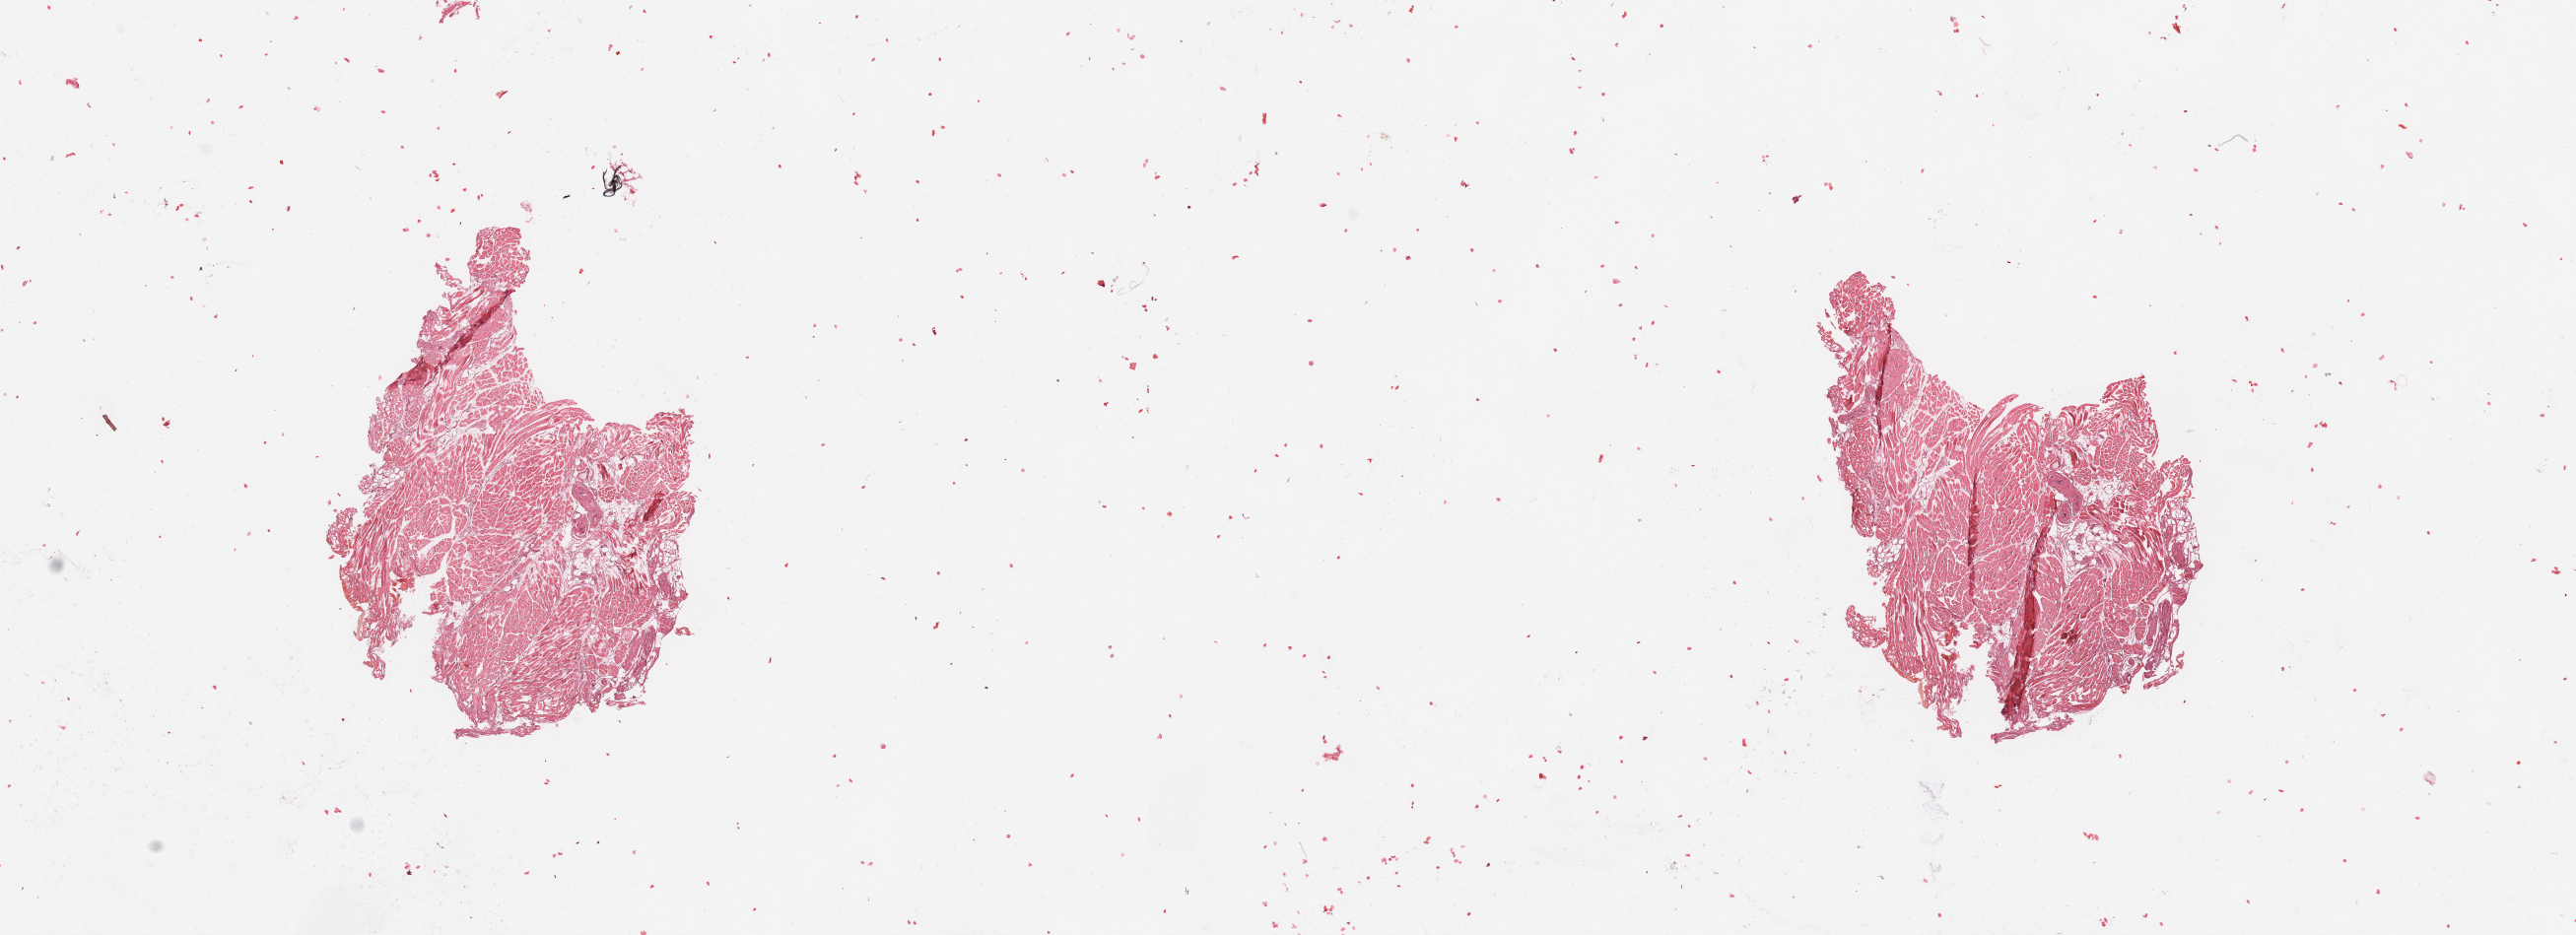
Digitized Hematoxylin and eosin (H&E) stained tissue section (whole slide) — whole scanned area (about 20.7 x 7.5 mm, acquisition: 20x scan) shown as a low-resolution overview, head and neck, tissue type not recorded. Male, 53 y/o.
Patient diagnosis: Squamous cell carcinoma, NOS (tongue, NOS).